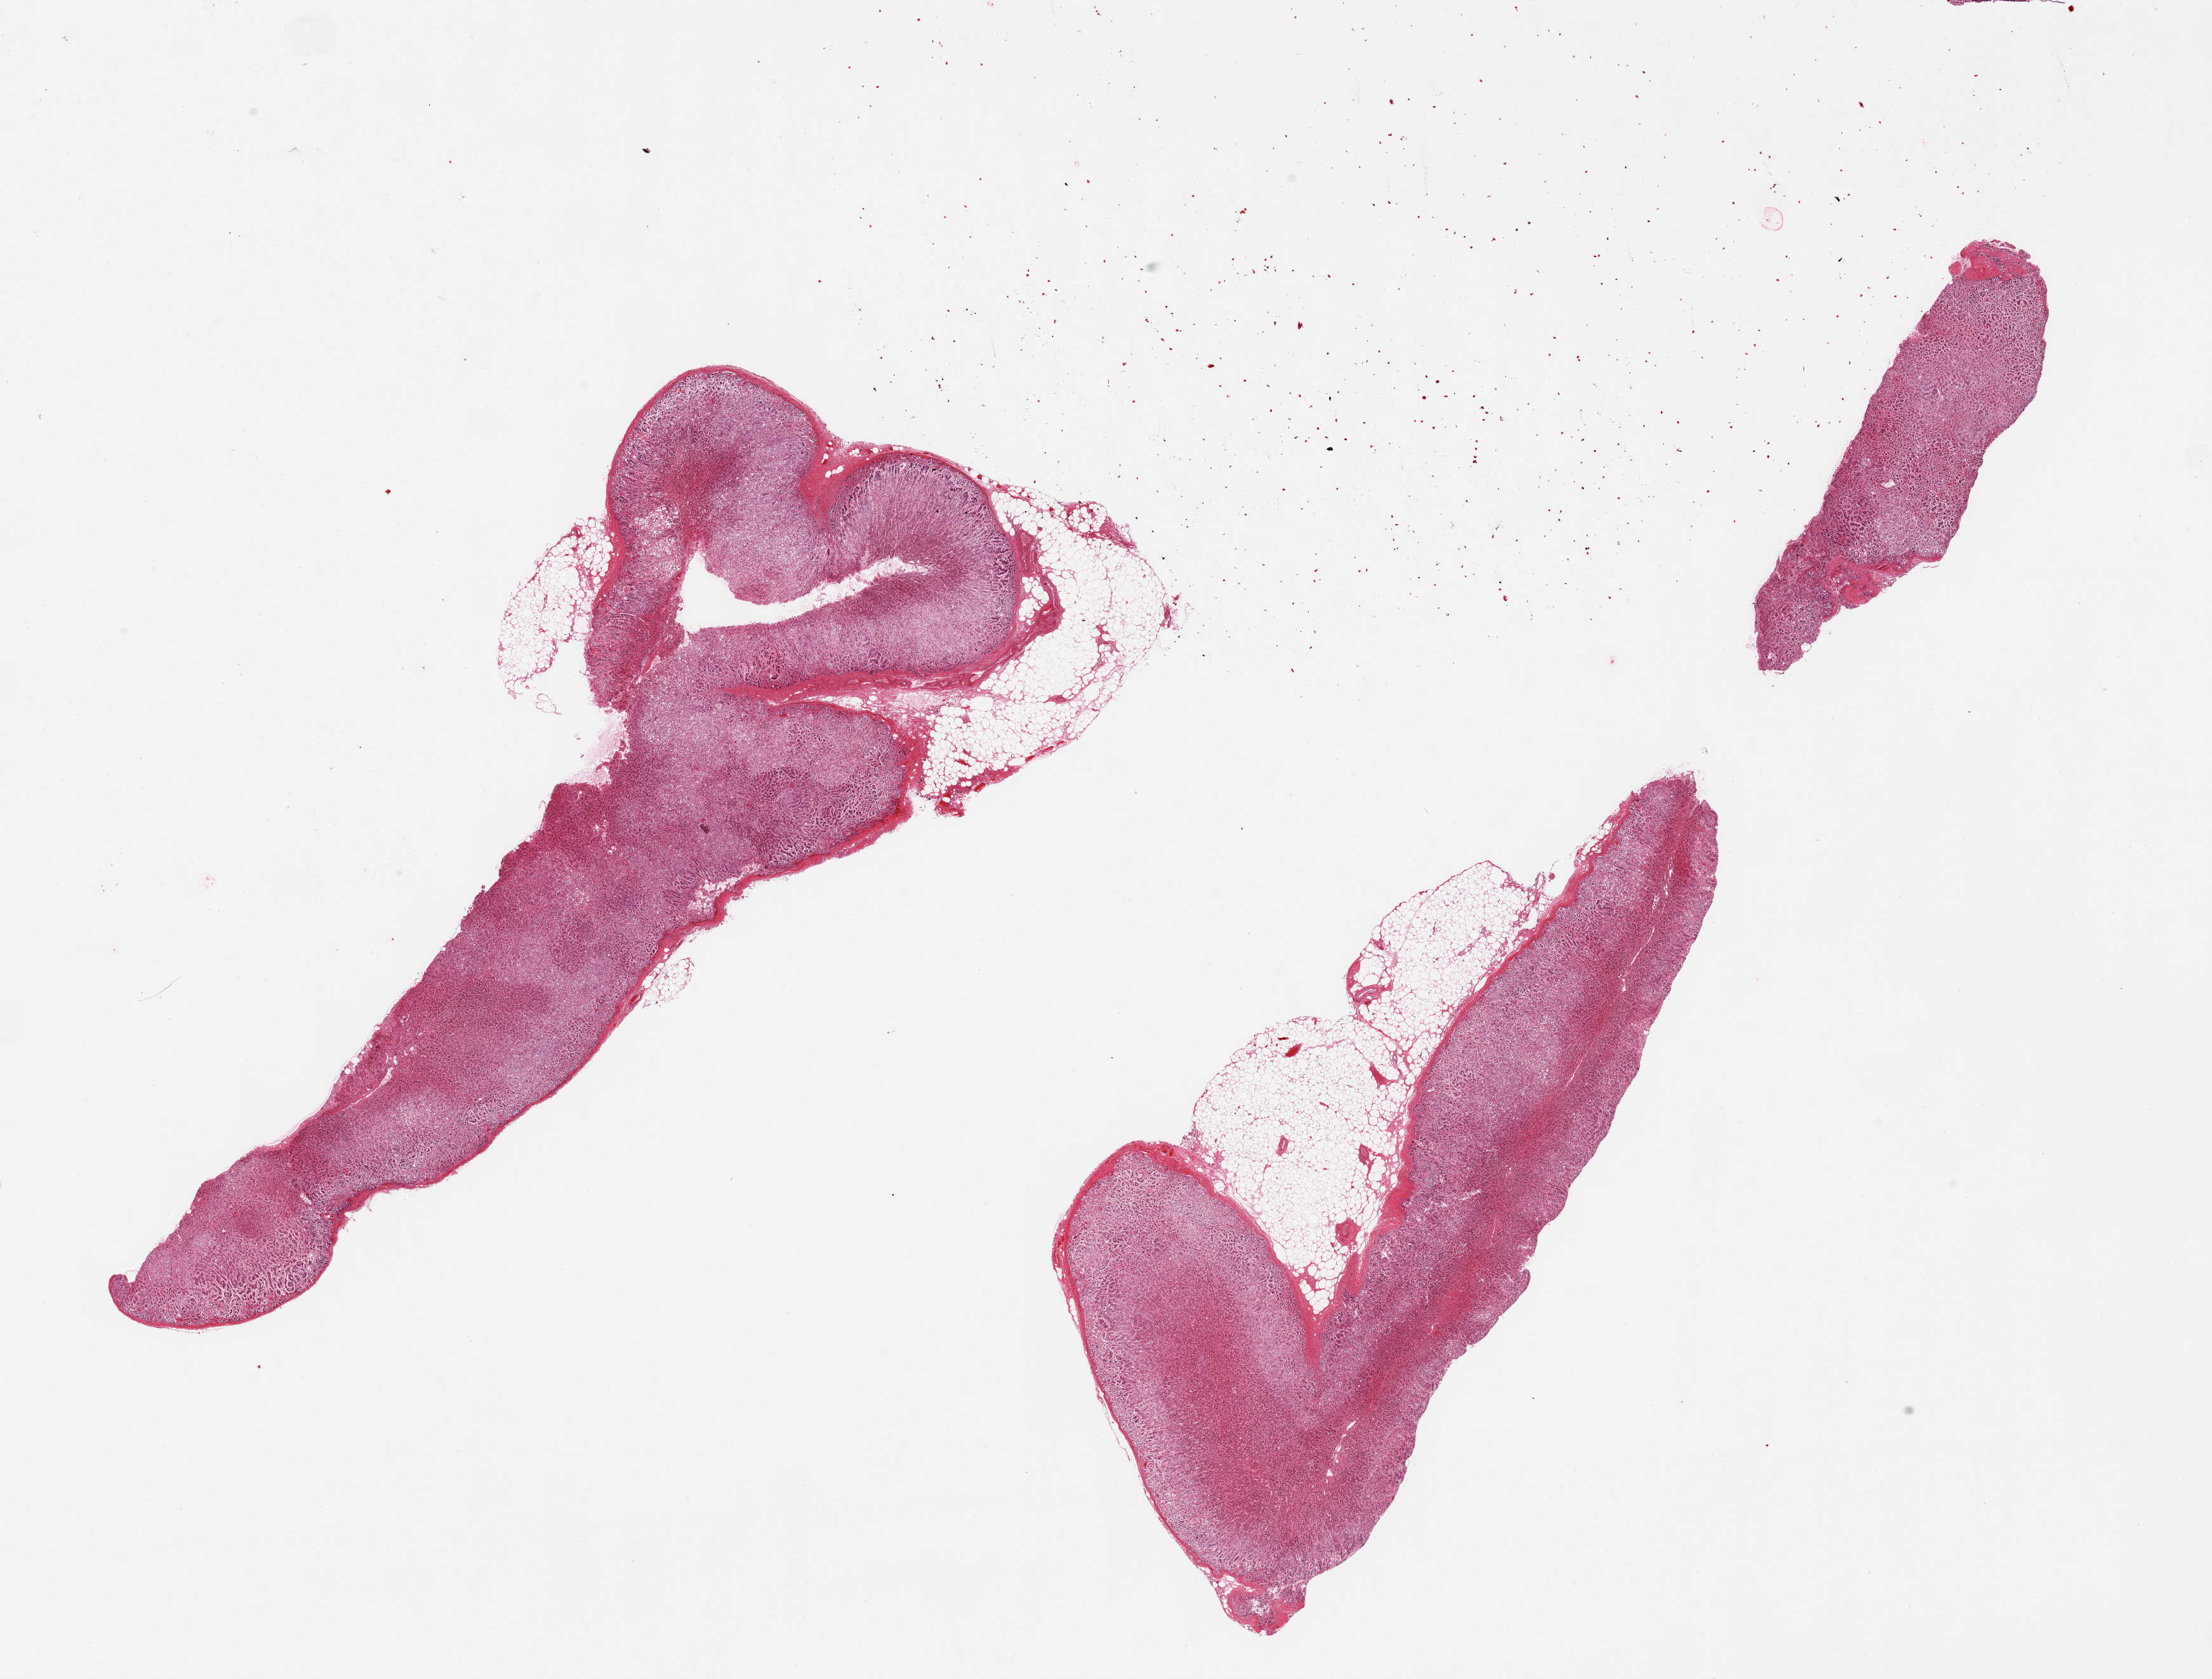
Whole-slide image, H&E stain, brightfield — low-resolution overview of the scanned area, about 27.6 x 20.9 mm (from a 20x scan). PAXgene-fixed paraffin-embedded (PFPE) section. Sampled site (target tissue): adrenal gland. Donor tissue sample.
Pathologist's review note for this sample: 2 pieces. 20 & 40% peripheral fat.